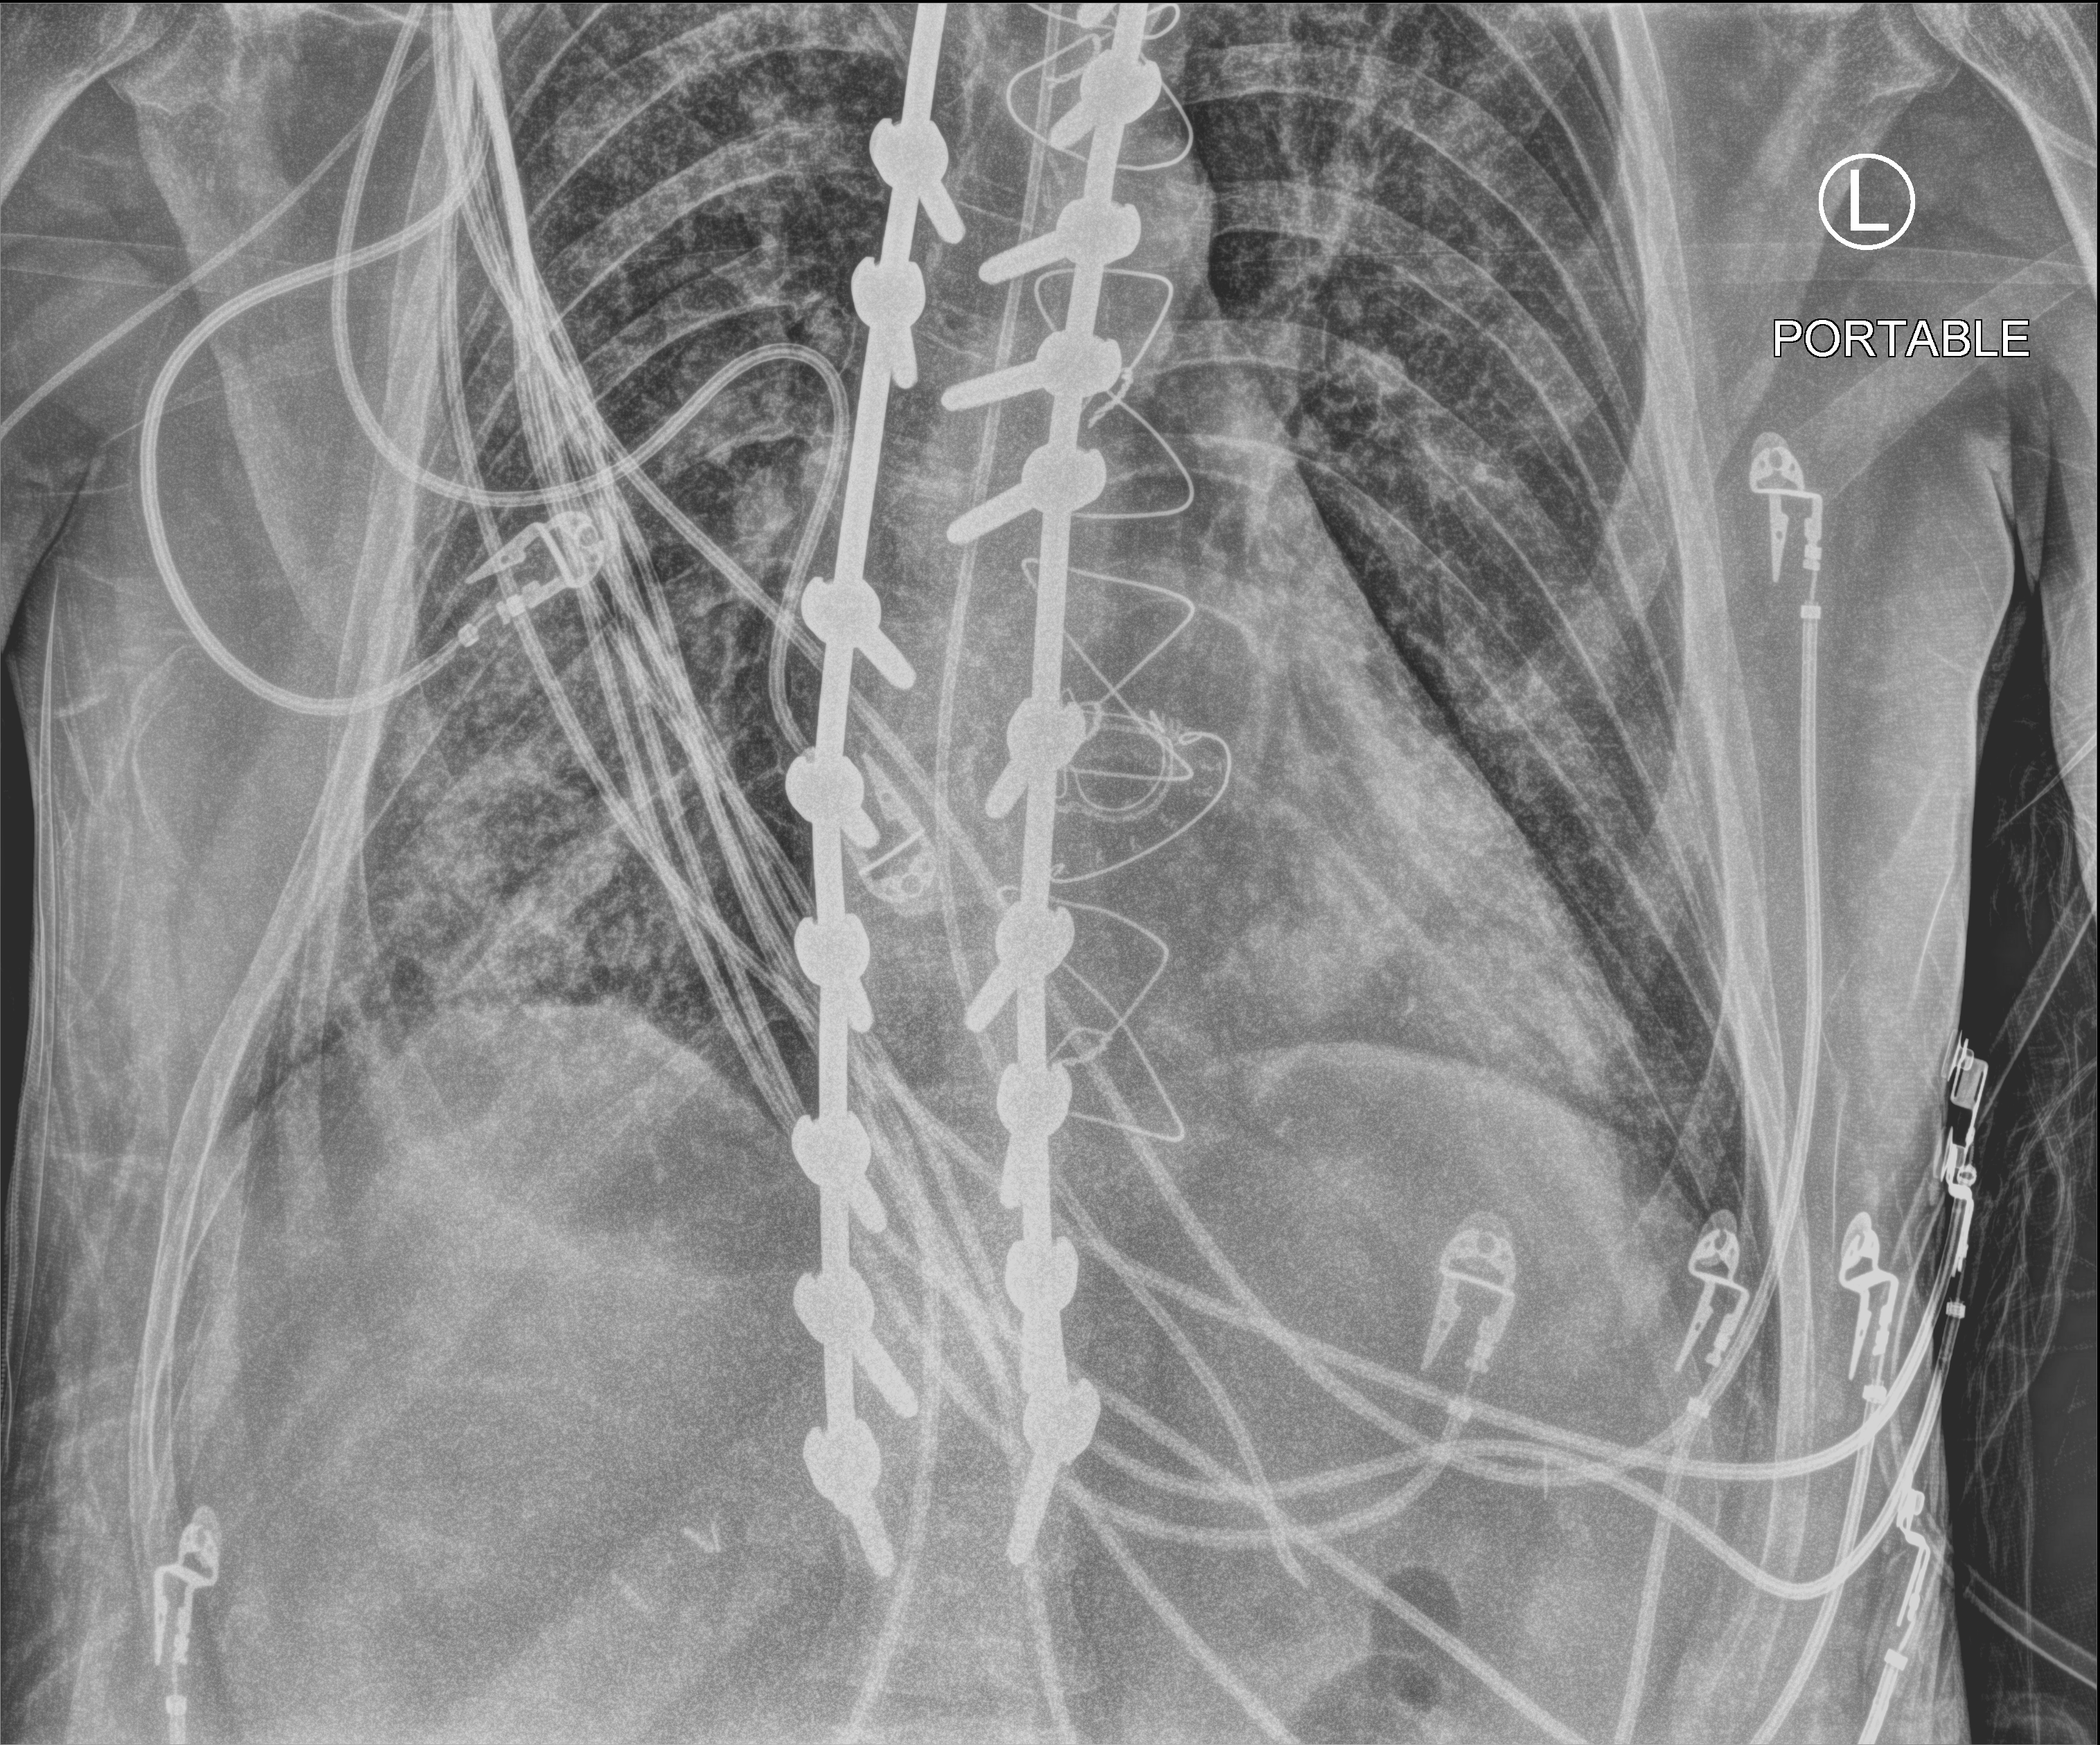
Bedside chest radiograph (computed radiography); anteroposterior (AP) projection. Adult patient hospitalised with COVID-19, age 18–59 years.
Admission-level facts for this patient (not findings on this image; timing relative to this image not recorded): admitted to intensive care during this hospital stay: yes.